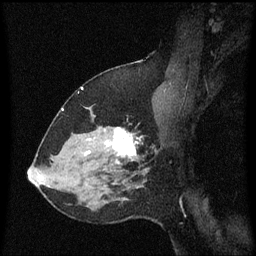
Breast MRI (dynamic contrast-enhanced), one sagittal slice; position 41 of 60 along the scan axis; dynamic contrast-enhanced series, image 2 of 3 at this slice position (ordered by acquisition); 1.5 T; TE 4.2 ms, TR 8.4 ms; 2 mm slice thickness; 256 × 256 image matrix, field of view 200 × 200 mm. Patient: female, 37 years. Case-level facts recorded for this patient, not image findings: setting: breast cancer imaged before/during neoadjuvant chemotherapy; receptor status: HR-positive, HER2-negative.
Structures marked on this image (semi-automatically segmented with operator editing):
- analysis volume of interest (the breast-tissue region the enhancement analysis was run in; not a lesion): bounding box (x1, y1, x2, y2) in pixels: (95, 110, 157, 171)
- tumour enhancement mask (voxels above the 70 % enhancement threshold inside the analysis volume of interest): (109, 128, 139, 163)